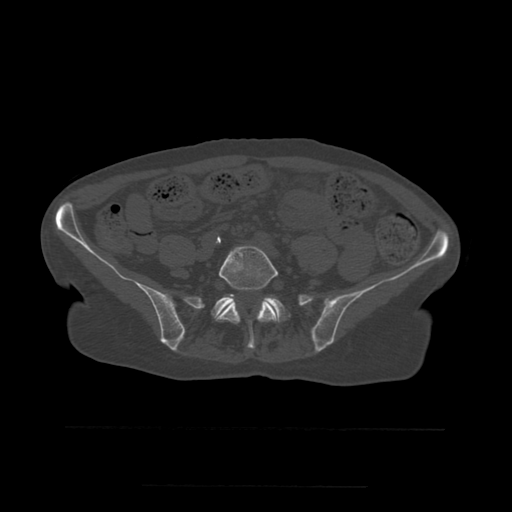
CT including the spine, one axial slice. Position 140 of 544 along the scan axis. Bone window (W 1800 / L 400 HU). 512 × 512 image matrix, field of view 350 × 350 mm. Patient age 58 years. From the clinical record (not read from this slice): primary cancer: lung.
Annotated regions visible in this slice (semi-automatically segmented with operator editing):
- L5 vertebra: bounding box [x1, y1, x2, y2] px = [216, 246, 279, 349]